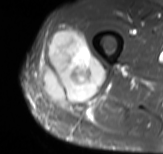
MRI of an extremity soft-tissue mass, one axial slice. Position 36 of 61 along the scan axis. STIR. MR volume resampled by the dataset authors to the PET/CT grid (not the native acquisition matrix). 3.27 mm slice thickness. 163 × 154 image matrix. Male patient. Case-level facts recorded for this patient, not image findings: histological type: poorly differentiated synovial sarcoma; grade: high; site of the primary tumour: right buttock.
Structures marked on this image (expert contour drawn on MRI and transferred to this co-registered scan by the dataset authors):
- gross tumour volume including surrounding oedema: bounding box (x1, y1, x2, y2) in pixels: (41, 30, 104, 109)
- gross tumour volume (mass): (41, 30, 104, 109)